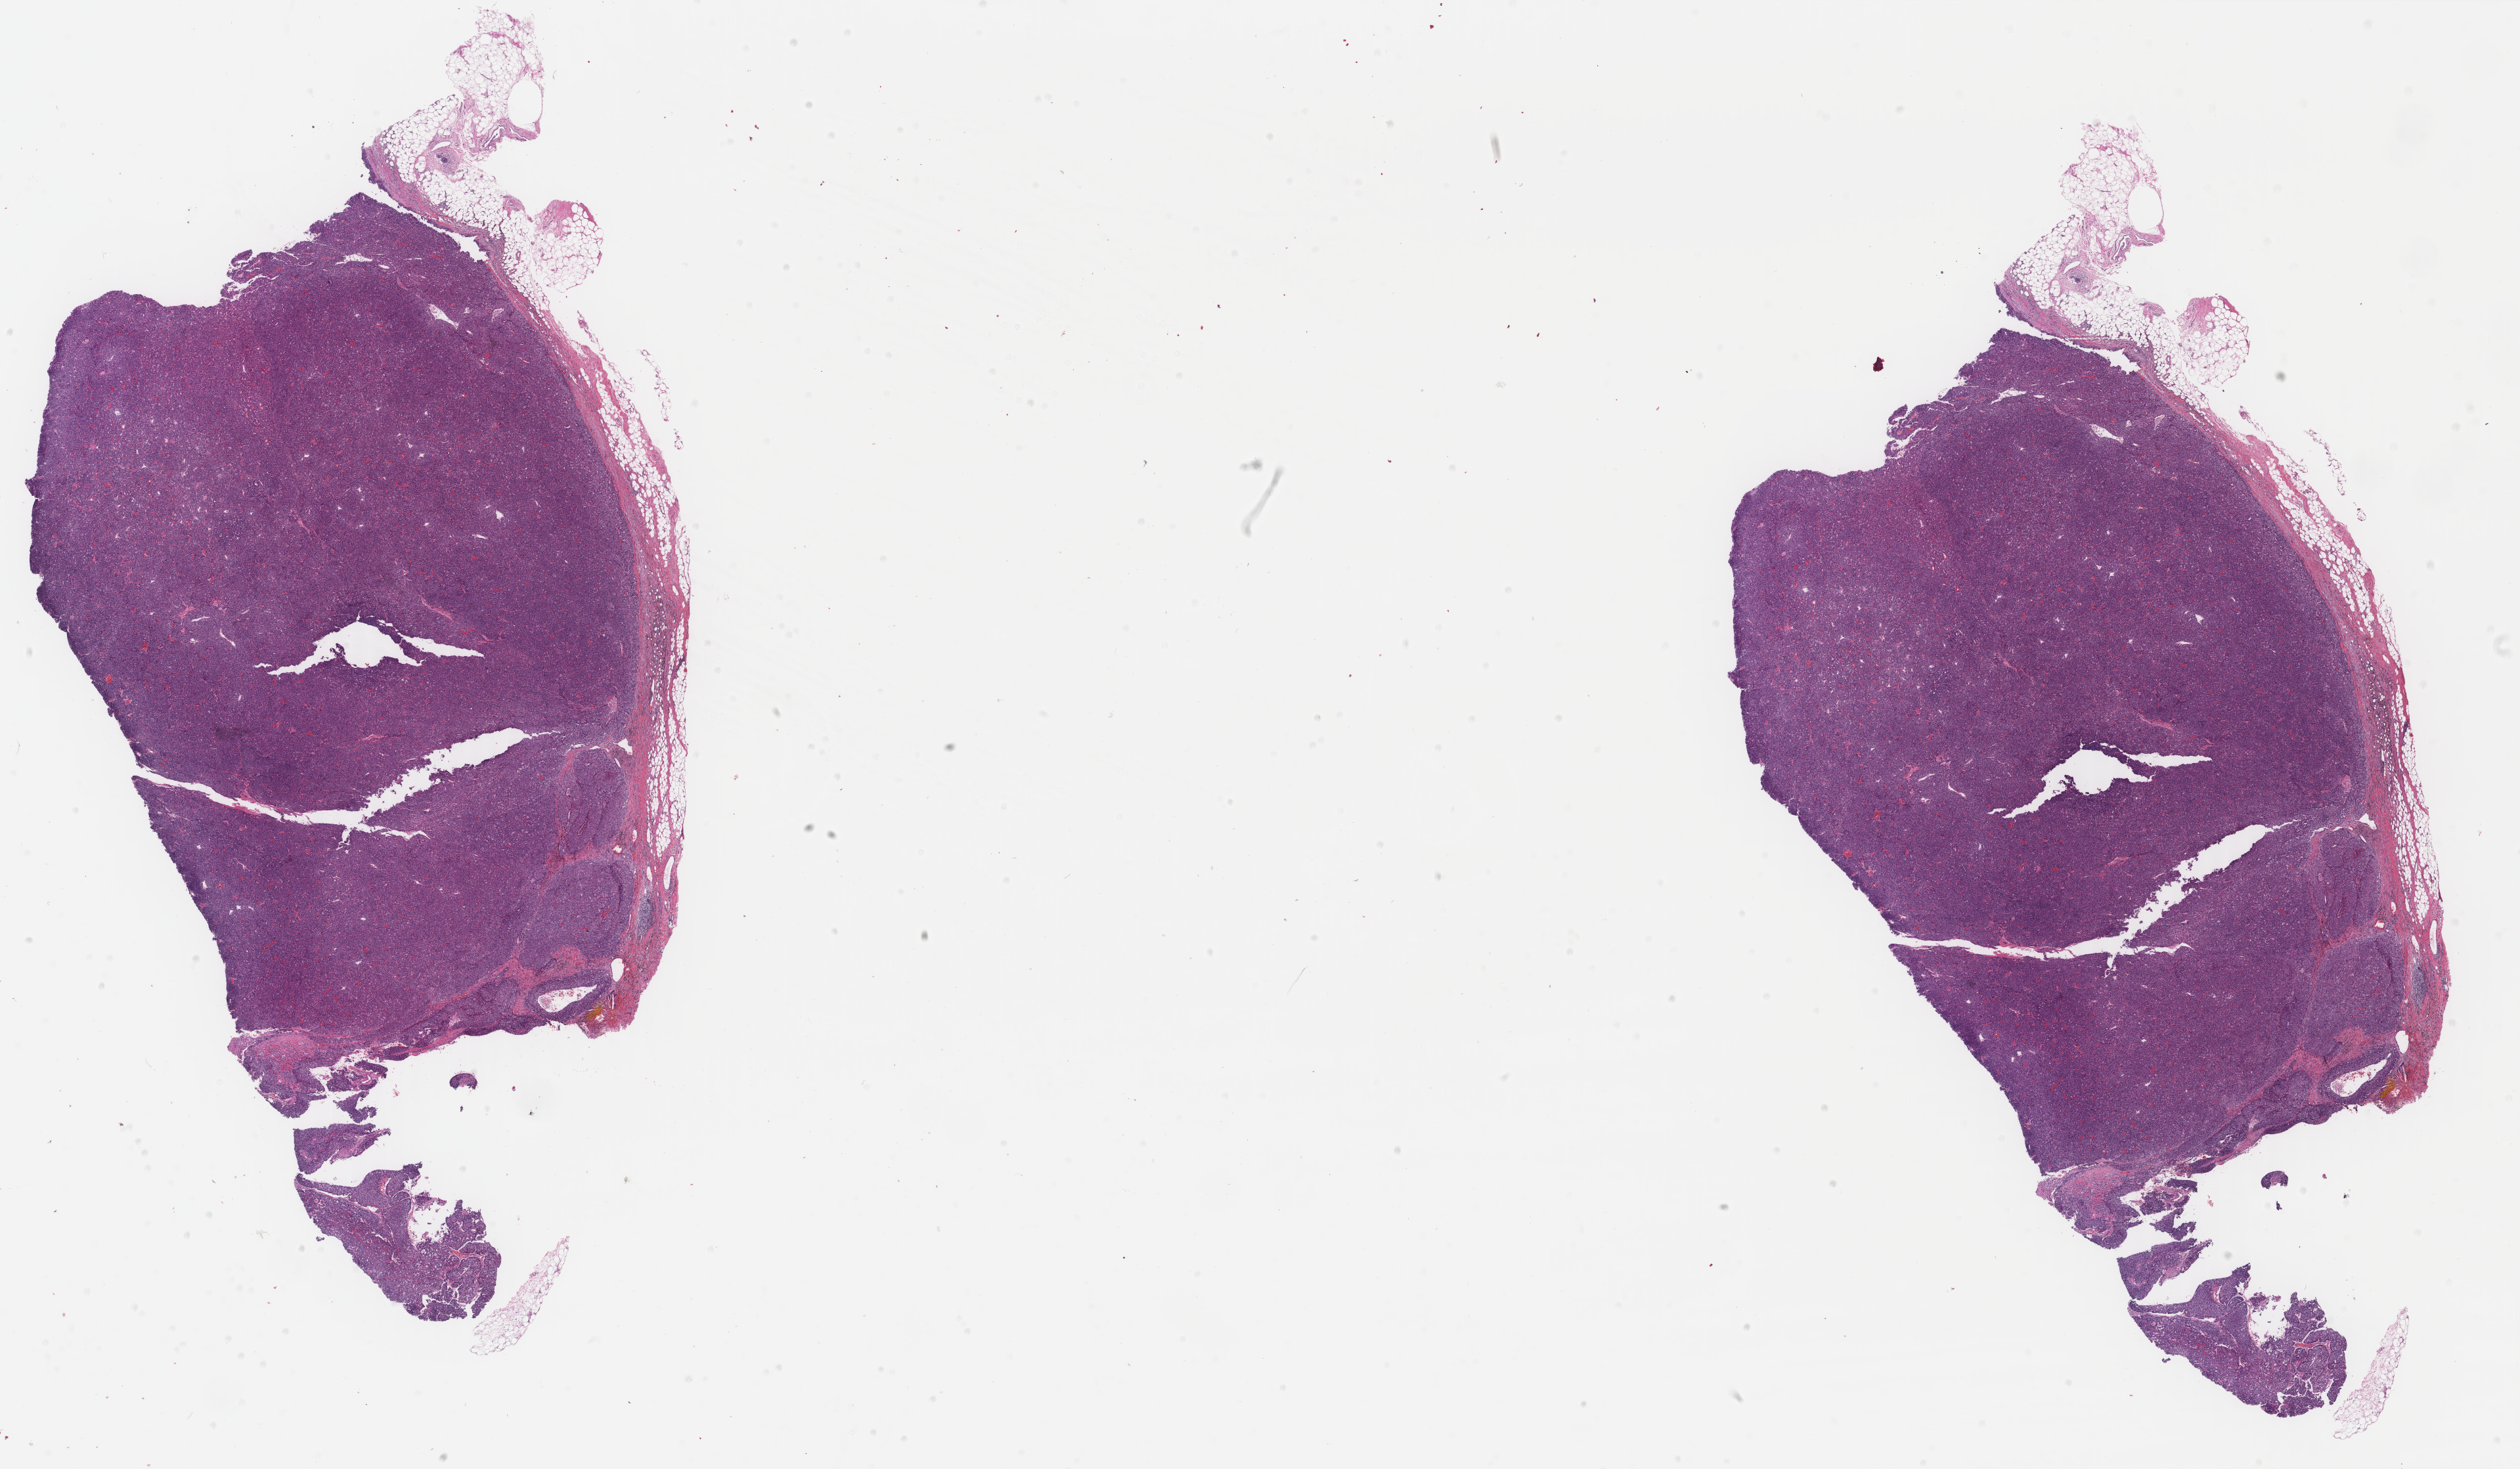
H&E whole-slide image — a low-resolution overview of the entire scanned area, about 30.5 x 17.8 mm (acquisition: 40x scan); formalin-fixed paraffin-embedded (FFPE) diagnostic section; breast, primary tumour sample. Patient: female, age at initial diagnosis 62 years.
Diagnosis: Infiltrating duct carcinoma, NOS.